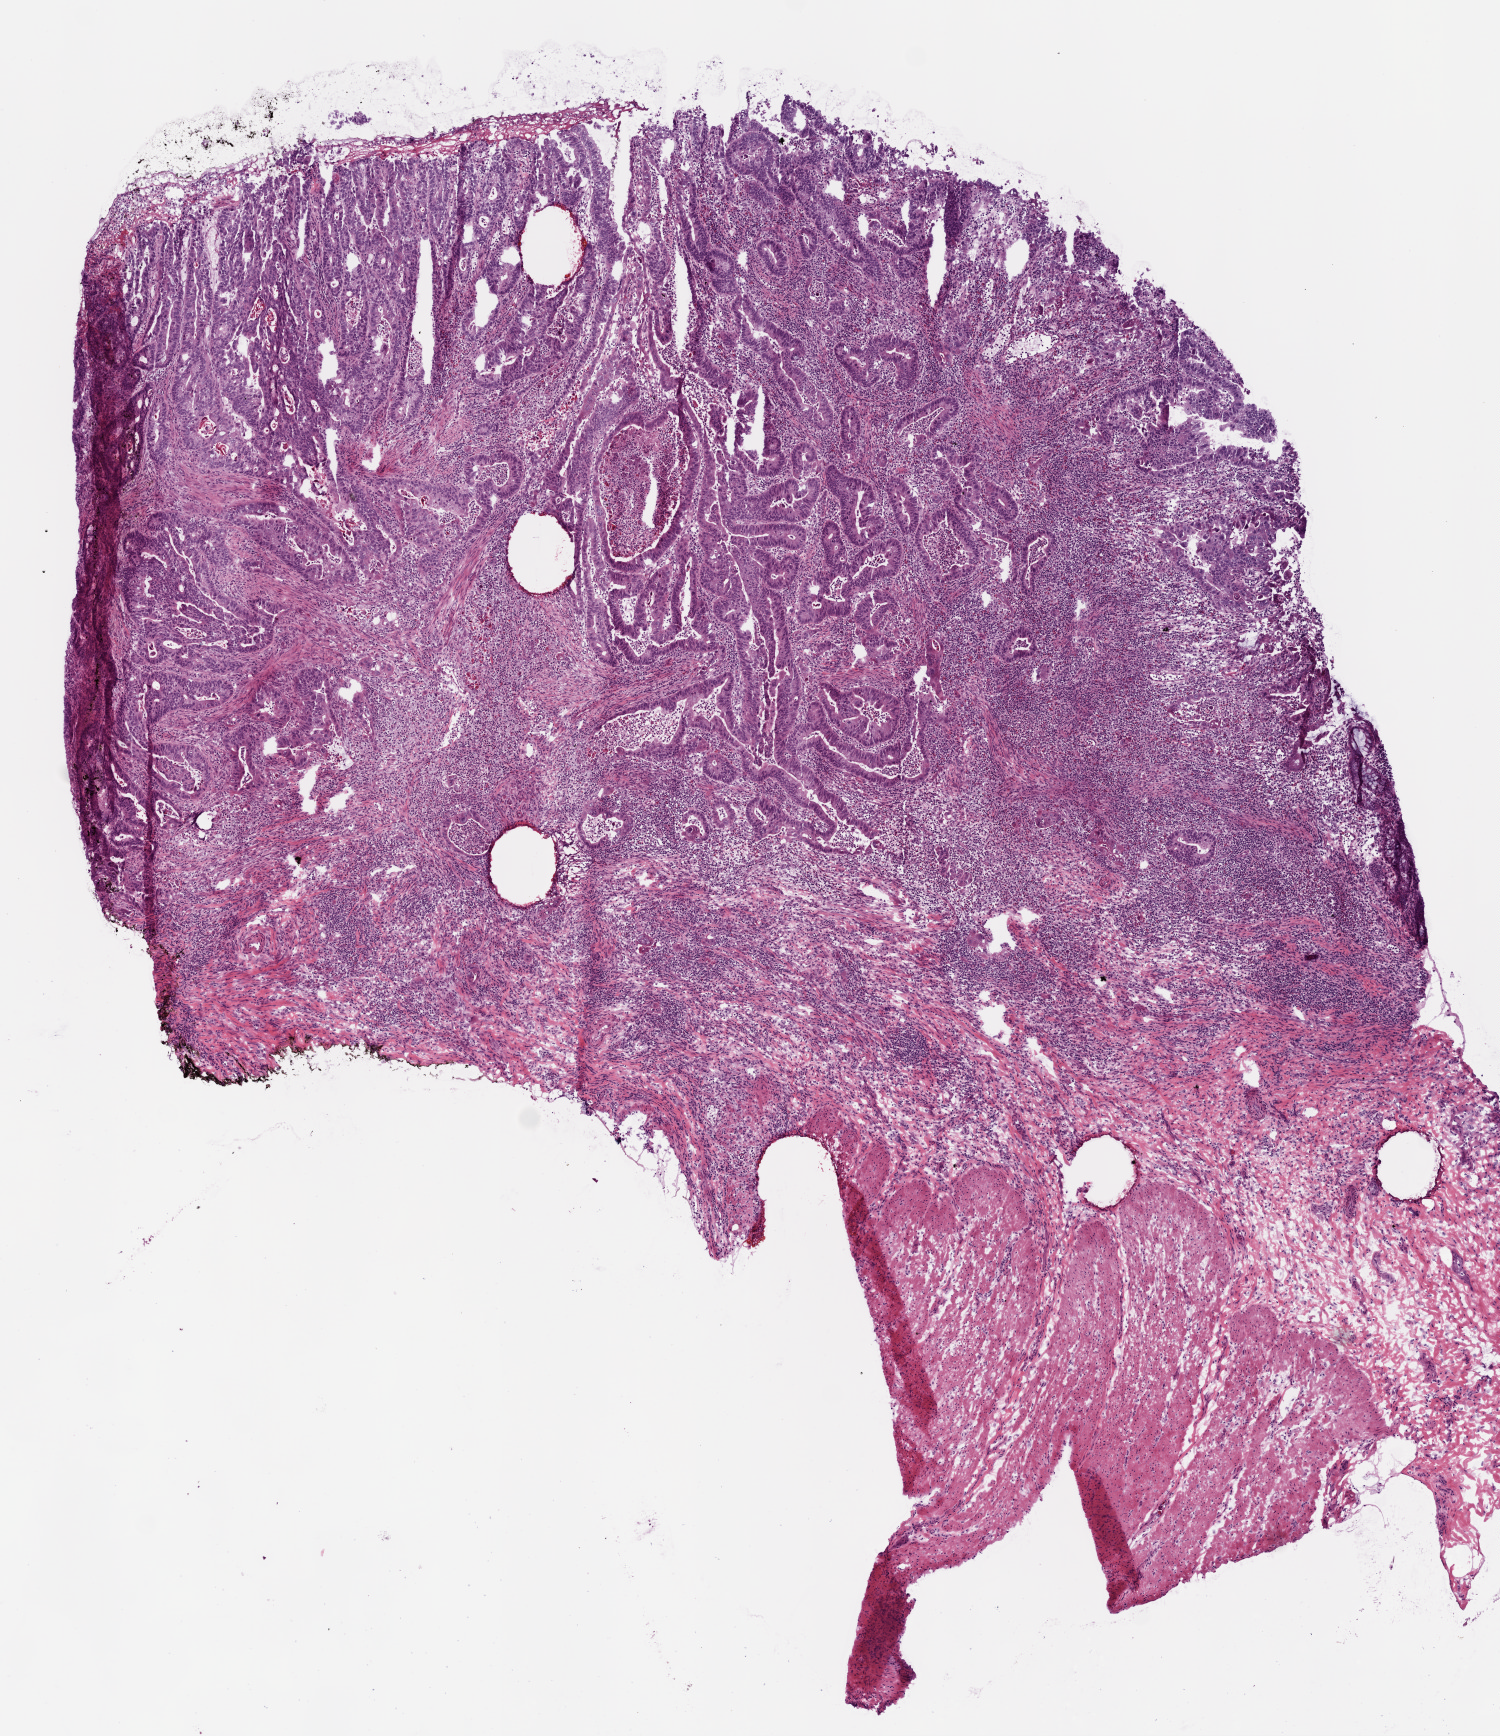
Whole-slide histology image, H&E — a low-resolution overview of the entire scanned area, about 6.0 x 7.0 mm, frozen section from the top of the tissue portion, sample: primary tumour, colon. Male, age 58 years at initial diagnosis. Slide review estimates, as recorded: tumour cells 65%, tumour nuclei 70%, normal cells 0%, stromal cells 25%, necrosis 10%. Infiltration values recorded for this section: lymphocyte infiltration 20%.
Histologic diagnosis: Adenocarcinoma, NOS (ascending colon).